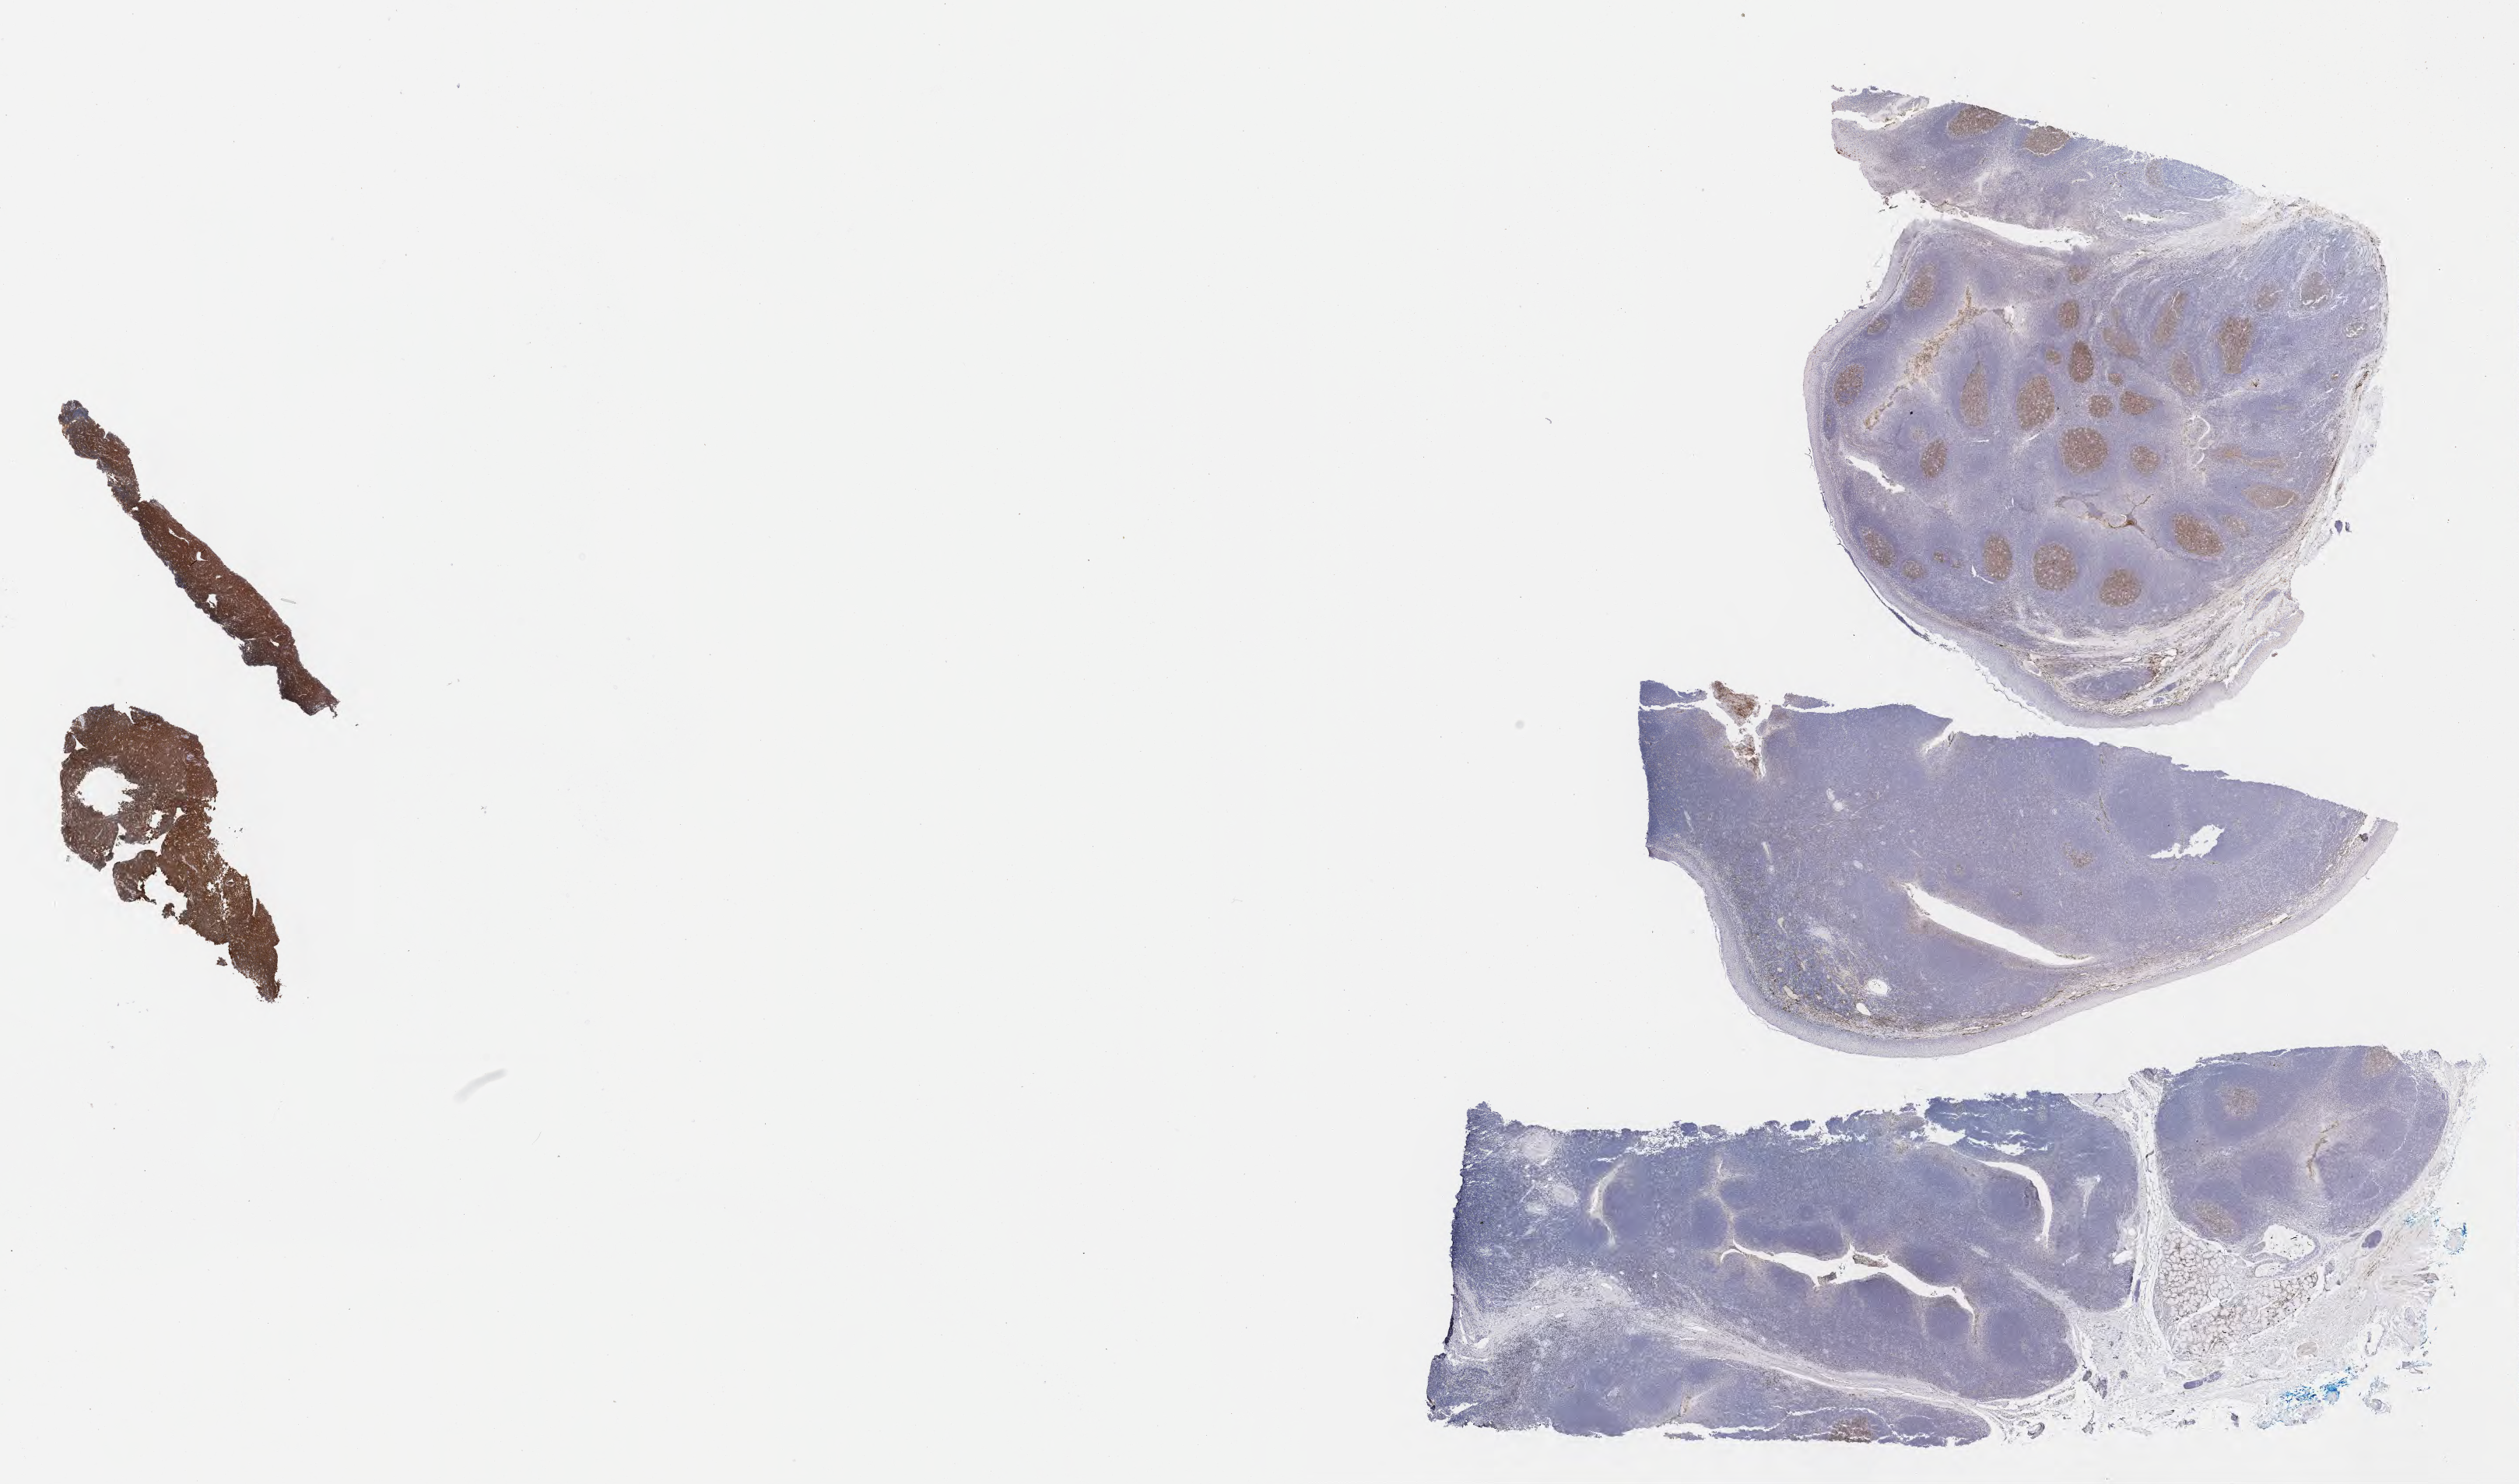
Immunohistochemistry (IHC) whole-slide image stained for CD10 — a low-resolution overview of the entire scanned area, about 26.2 x 15.4 mm, specimen: tumor tissue. Male, age 8 years at initial diagnosis.
* diagnosis: Burkitt lymphoma, NOS